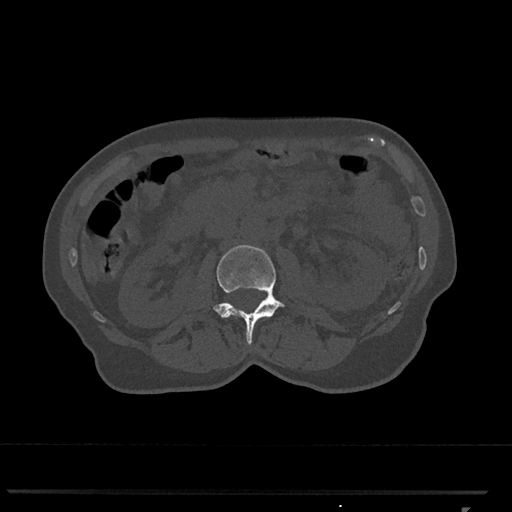
CT including the spine, one axial slice; slice 335 of 793 in the series (ordered by position); bone window (W 1800 / L 400 HU); 512 × 512 image matrix. Patient: female, 62 years. Case-level facts recorded for this patient, not image findings: primary cancer: renal.
Annotated regions visible in this slice (semi-automatically segmented with operator editing):
- L2 vertebra: bounding box <213,245,285,345> (left, top, right, bottom; pixels)